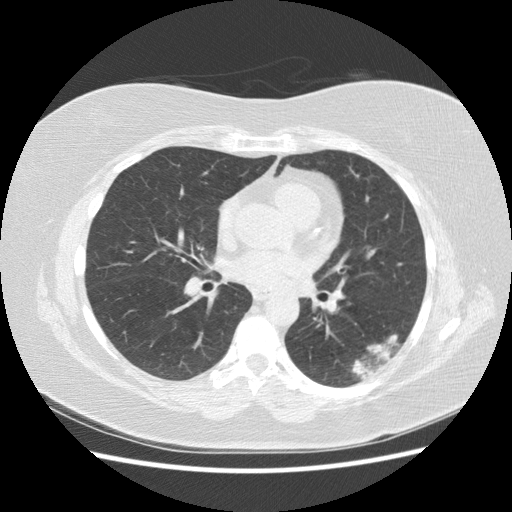
Axial slice from a low-dose chest CT screening exam. Third annual screen. Lung window (W 1500 / L -600 HU). 2.5 mm slice thickness. Slice 79 of 151 in the series. Female participant, aged 57 years at enrolment. Current smoker at enrolment.
Lesion marked by an expert reader, bounding box [x1, y1, x2, y2] px = [335, 324, 409, 387]. The exam's reader record, not a measurement of the box and not confirmed to be the same lesion: non-calcified nodule or mass ≥4 mm, left lower lobe, 40 × 20 mm, poorly defined margins, mixed attenuation, pre-existing on the prior screen: yes; interval growth: yes. Later outcome: lung cancer diagnosed 55 days after this screen — squamous cell carcinoma, NOS, left lower lobe, poorly differentiated (G3), stage IB (AJCC 6th edition), 40 mm at pathology.